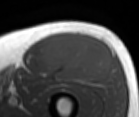
MRI of an extremity soft-tissue mass, one axial slice; position 50 of 86 along the scan axis; MR volume resampled by the dataset authors to the PET/CT grid (not the native acquisition matrix); 139 × 117 image matrix. Male patient. From the clinical record (not read from this slice): histological type: extraskeletal osteosarcoma; grade: high; site of the primary tumour: thigh.
Outlined on this slice (expert contour drawn on MRI and transferred to this co-registered scan by the dataset authors):
- gross tumour volume (mass): bounding box [x1, y1, x2, y2] px = [42, 34, 112, 83]